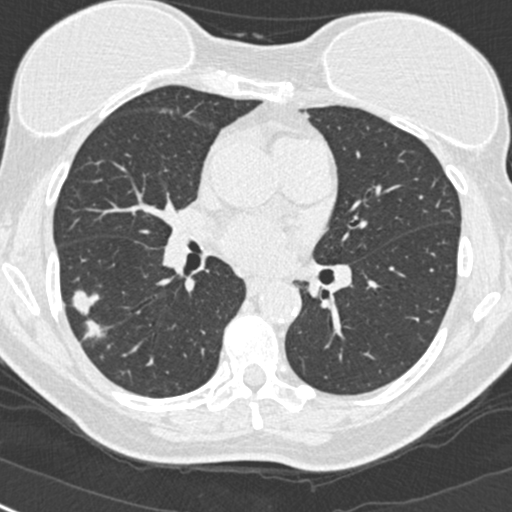
Low-dose screening chest CT, one axial slice; position 139 of 268 along the scan axis; reconstruction kernel B30f; lung window (W 1500 / L -600 HU); 1 mm slice thickness; 512 × 512 image matrix, field of view 296 × 296 mm.
Structures marked on this image (expert manual segmentation):
- lesion 1 (tumor, upper lobe of right lung): bounding box <72,290,105,339> (left, top, right, bottom; pixels)